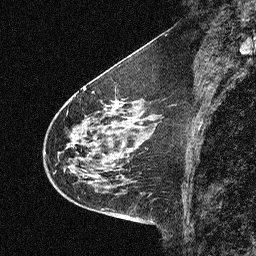
Breast MRI (dynamic contrast-enhanced), one sagittal slice. Dynamic contrast-enhanced study with each time point stored as its own series, time point 2 of 3 at this slice position (early post-contrast, ordered by acquisition time). 1.5 T. TE 4.5 ms, TR 11 ms. 2.06 mm slice thickness. 256 × 256 image matrix, field of view 200 × 200 mm. Female patient, age 46 years. Case-level facts recorded for this patient, not image findings: setting: breast cancer imaged before/during neoadjuvant chemotherapy; receptor status: HER2-positive.
Outlined on this slice (semi-automatic segmentation, software-assisted and operator-edited):
- analysis volume of interest (the breast-tissue region the enhancement analysis was run in; not a lesion): bounding box [x1, y1, x2, y2] px = [42, 80, 150, 180]
- tumour enhancement mask (voxels above the 90 % enhancement threshold inside the analysis volume of interest): [58, 92, 136, 168]